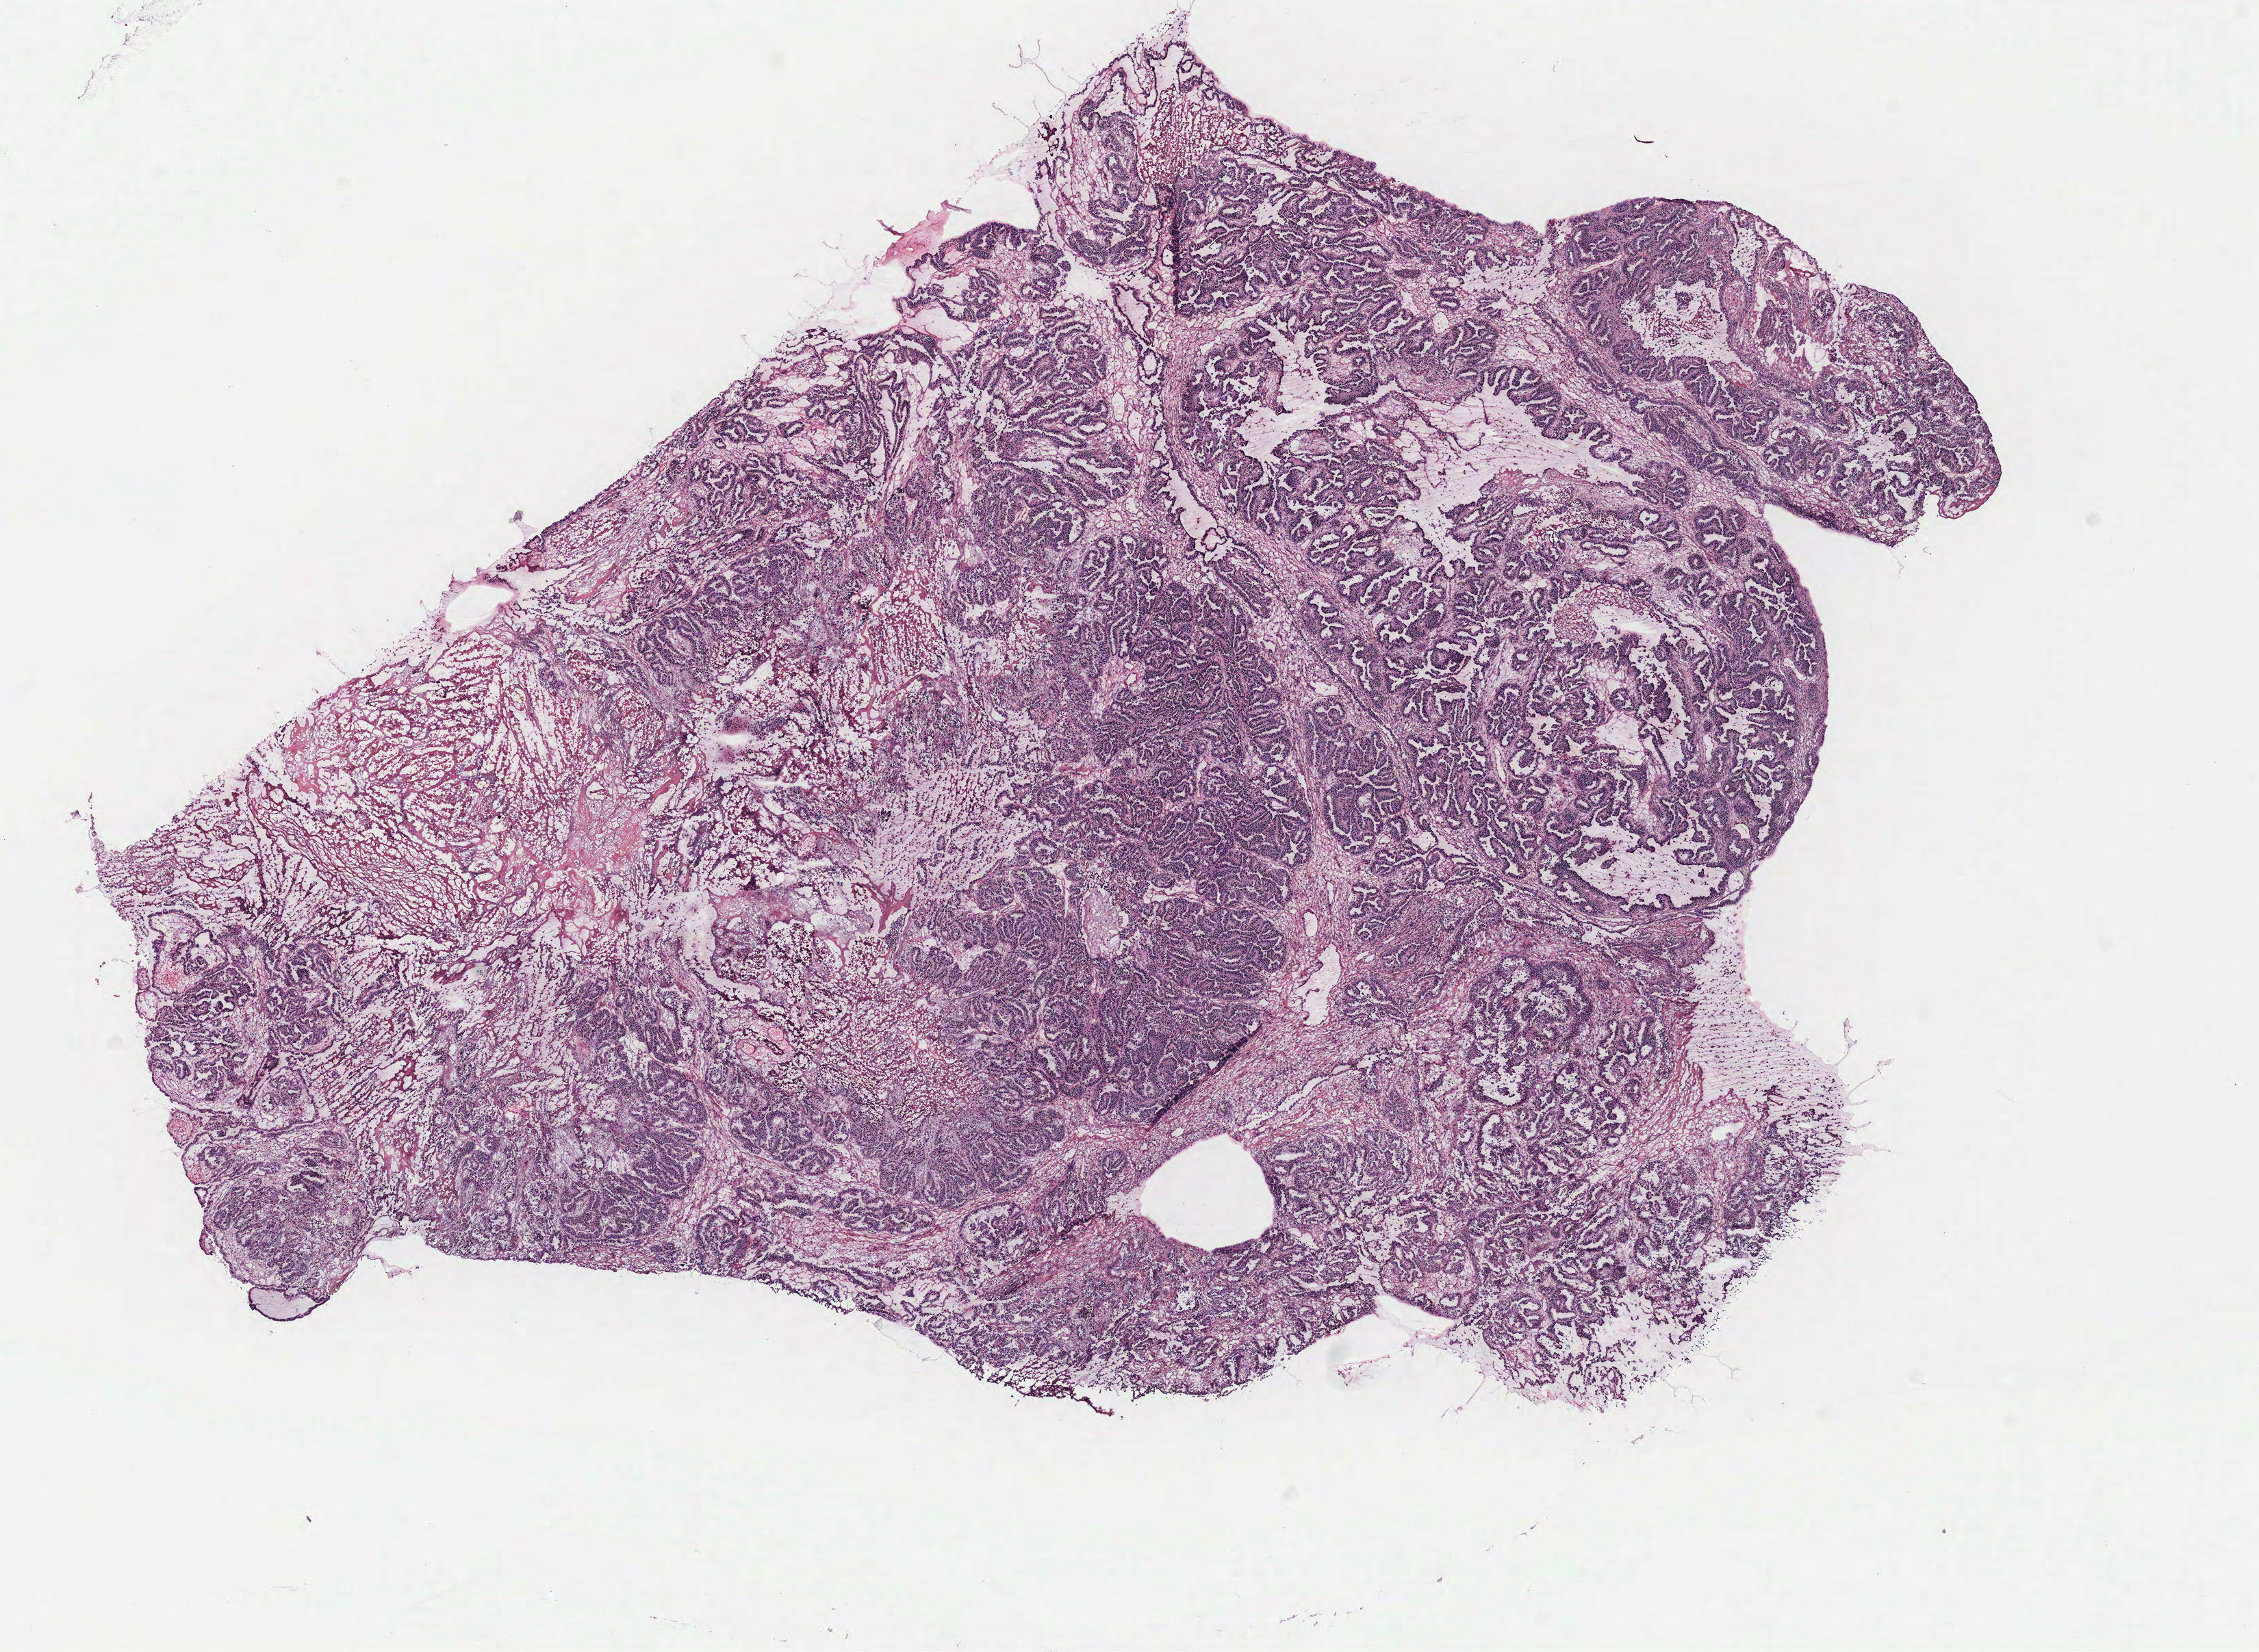
Hematoxylin and eosin (H&E) stained whole-slide image, a low-resolution overview of the entire scanned area, about 13.2 x 9.7 mm; tumour tissue sample, ovary. Patient: female, age 55 years.
Primary tumour site (as recorded): fallopian tube. Histologic diagnosis: Serous adenocarcinoma, NOS (fallopian tube).